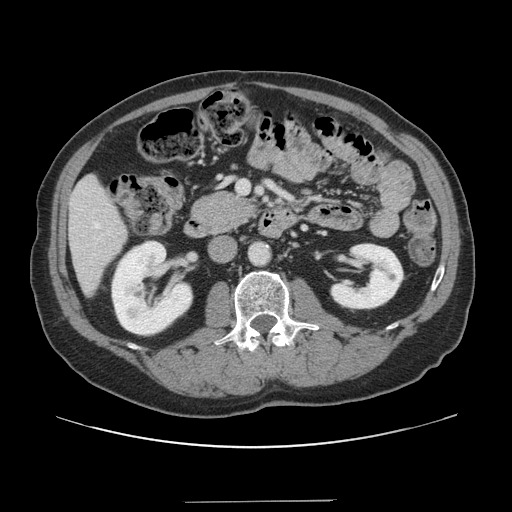
Contrast-enhanced abdominal CT, one axial slice; intravenous contrast given; soft-tissue window (W 400 / L 40 HU); 2.5 mm slice thickness; 512 × 512 image matrix, field of view 399 × 399 mm. Male patient, age 63 years. From the clinical record (not read from this slice): diagnosis: colorectal cancer liver metastases, imaged before liver resection; multiple liver metastases: no; largest metastasis: 2.1 cm; disease in both lobes: no.
Outlined on this slice (outlined manually by an expert reader):
- hepatic veins: bounding box <95,224,99,228> (left, top, right, bottom; pixels)
- liver: <70,177,127,293>
- planned liver remnant (the part of the liver to remain after resection): <70,177,127,293>
- portal vein (with intrahepatic branches): <237,181,249,193>